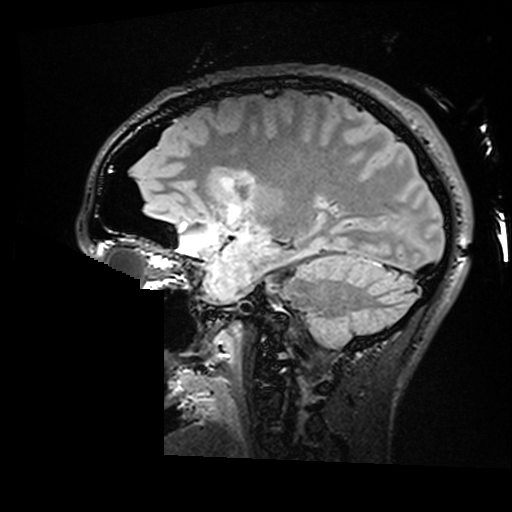
Brain MRI from a brain-tumour surgery series, one sagittal slice; slice 106 of 176 in the series (ordered by position); T2 FLAIR; 512 × 512 image matrix, field of view 250 × 250 mm. From the clinical record (not read from this slice): histopathology: Astrocytoma; WHO grade: 2.
Structures marked on this image (outlined manually by an expert reader):
- residual tumour: bounding box <221,176,235,188> (left, top, right, bottom; pixels)